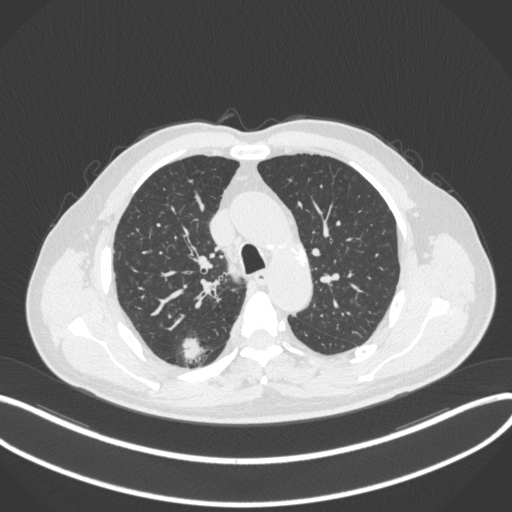
Chest CT, one axial slice; position 266 of 366 along the scan axis; reconstruction kernel B31f; 120 kVp; lung window (W 1500 / L -600 HU); 512 × 512 image matrix, field of view 400 × 400 mm. Male patient, age 69 years. Case-level facts recorded for this patient, not image findings: clinical TNM (as recorded): T1b N0 M0.
Structures marked on this image (rectangle marked by the reading radiologist):
- lung tumour (recorded histology: adenocarcinoma): box from (x=180, y=334) to (x=206, y=365) px